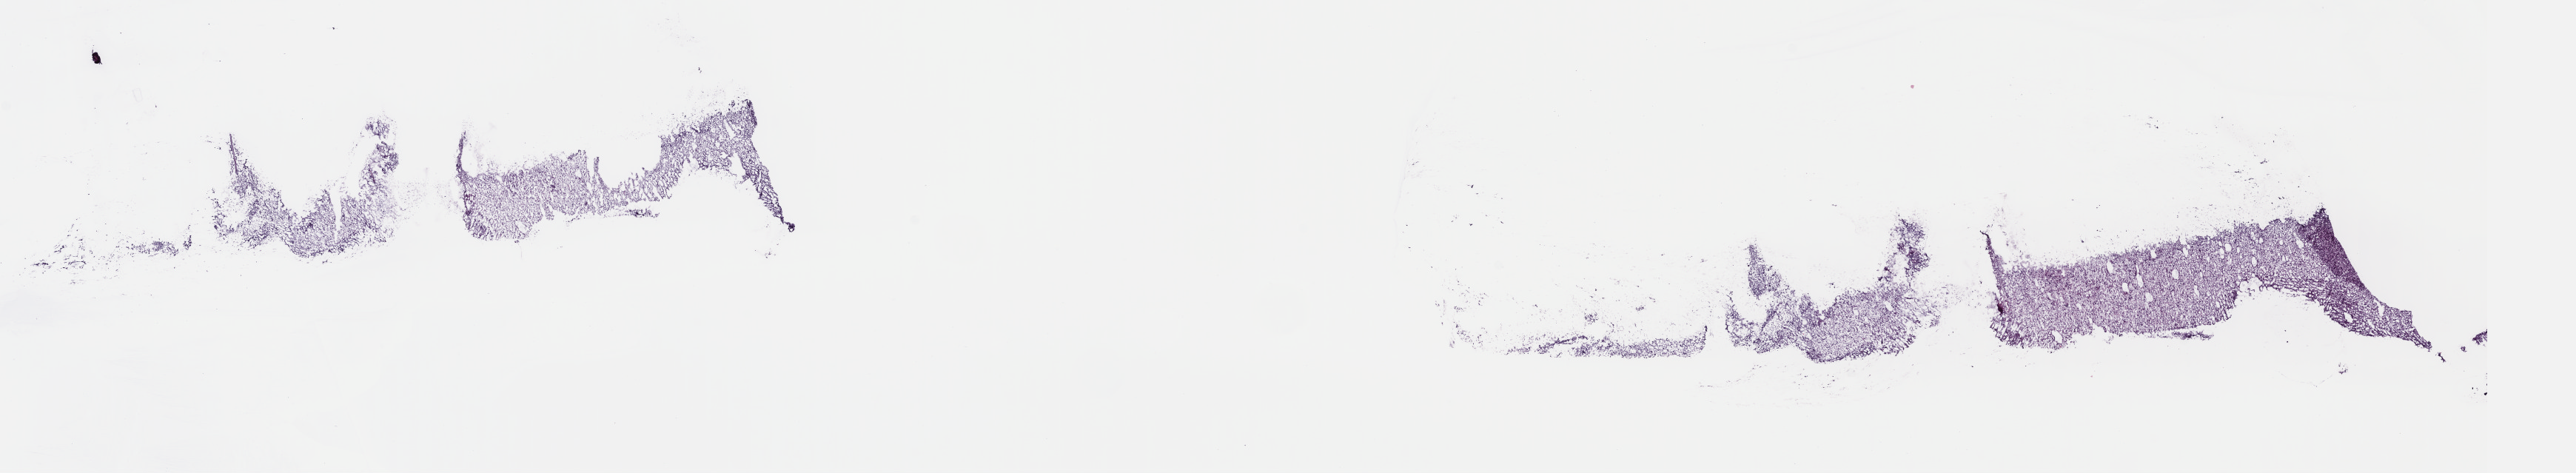
H&E whole-slide image — shown as a low-resolution overview of the whole scanned area (about 27.4 x 5.0 mm, from a 40x scan). Frozen section from the top of the tissue portion. Brain, primary tumour sample. Female, age 33 years at initial diagnosis. Histologic grade: G2 (moderately differentiated). Pathologist review of this section (percent, as recorded): tumour cells 80%, tumour nuclei 80%, normal cells 20%, stromal cells 0%, necrosis 0%. Inflammatory infiltration, as recorded: lymphocyte infiltration 0%, monocyte infiltration 0%, neutrophil infiltration 0%.
Diagnosis: Mixed glioma (temporal lobe). Laterality: left.